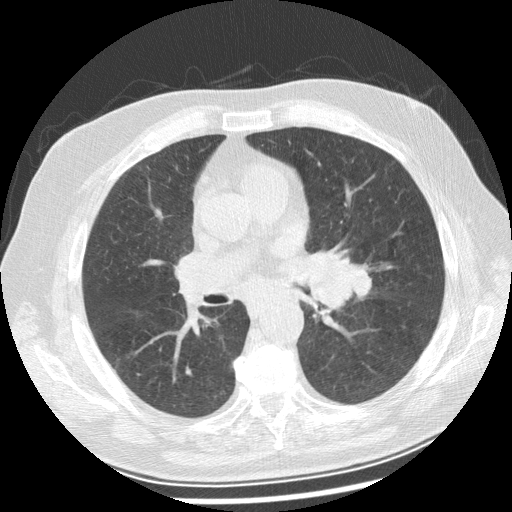
Low-dose screening chest CT, one axial slice. Position 139 of 250 along the scan axis. Lung window (W 1500 / L -600 HU). 512 × 512 image matrix.
Structures marked on this image (outlined manually by an expert reader):
- lesion 1 (tumor, left main bronchus): bounding box [x1, y1, x2, y2] px = [309, 263, 371, 307]